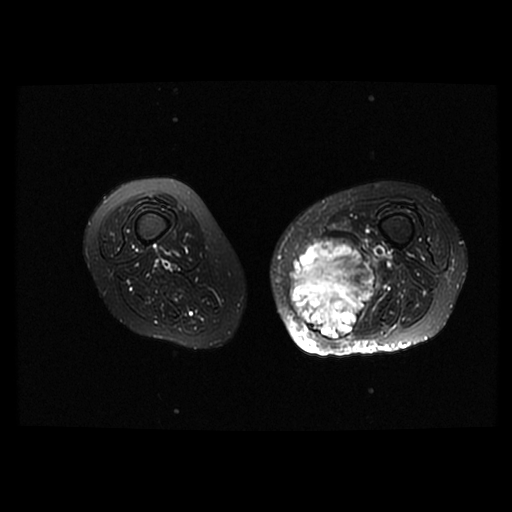
MRI of an extremity soft-tissue mass, one axial slice; slice 26 of 42 in the series (ordered by position); T2-weighted fat-saturated; 512 × 512 image matrix. Female patient. Case-level facts recorded for this patient, not image findings: histological type: pleomorphic leiomyosarcoma; grade: high; site of the primary tumour: left thigh.
Outlined on this slice (outlined manually by an expert reader):
- gross tumour volume including surrounding oedema: bounding box [x1, y1, x2, y2] px = [288, 239, 379, 340]
- gross tumour volume (mass): [288, 239, 375, 340]